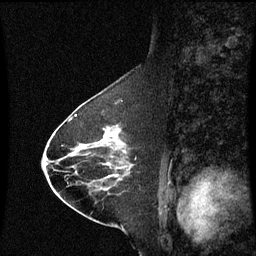
Breast MRI (dynamic contrast-enhanced), one sagittal slice; slice 32 of 60 in the series (ordered by position); dynamic contrast-enhanced series, image 2 of 3 at this slice position (ordered by acquisition); 1.5 T; TE 4.2 ms, TR 8.9 ms; 2 mm slice thickness; 256 × 256 image matrix, field of view 200 × 200 mm. Female patient, age 63 years. Case-level facts recorded for this patient, not image findings: setting: breast cancer imaged before/during neoadjuvant chemotherapy; receptor status: HR-positive, HER2-negative.
Annotated regions visible in this slice (semi-automatically segmented with operator editing):
- analysis volume of interest (the breast-tissue region the enhancement analysis was run in; not a lesion): bounding box (x1, y1, x2, y2) in pixels: (94, 124, 134, 177)
- tumour enhancement mask (voxels above the 70 % enhancement threshold inside the analysis volume of interest): (105, 132, 107, 137)